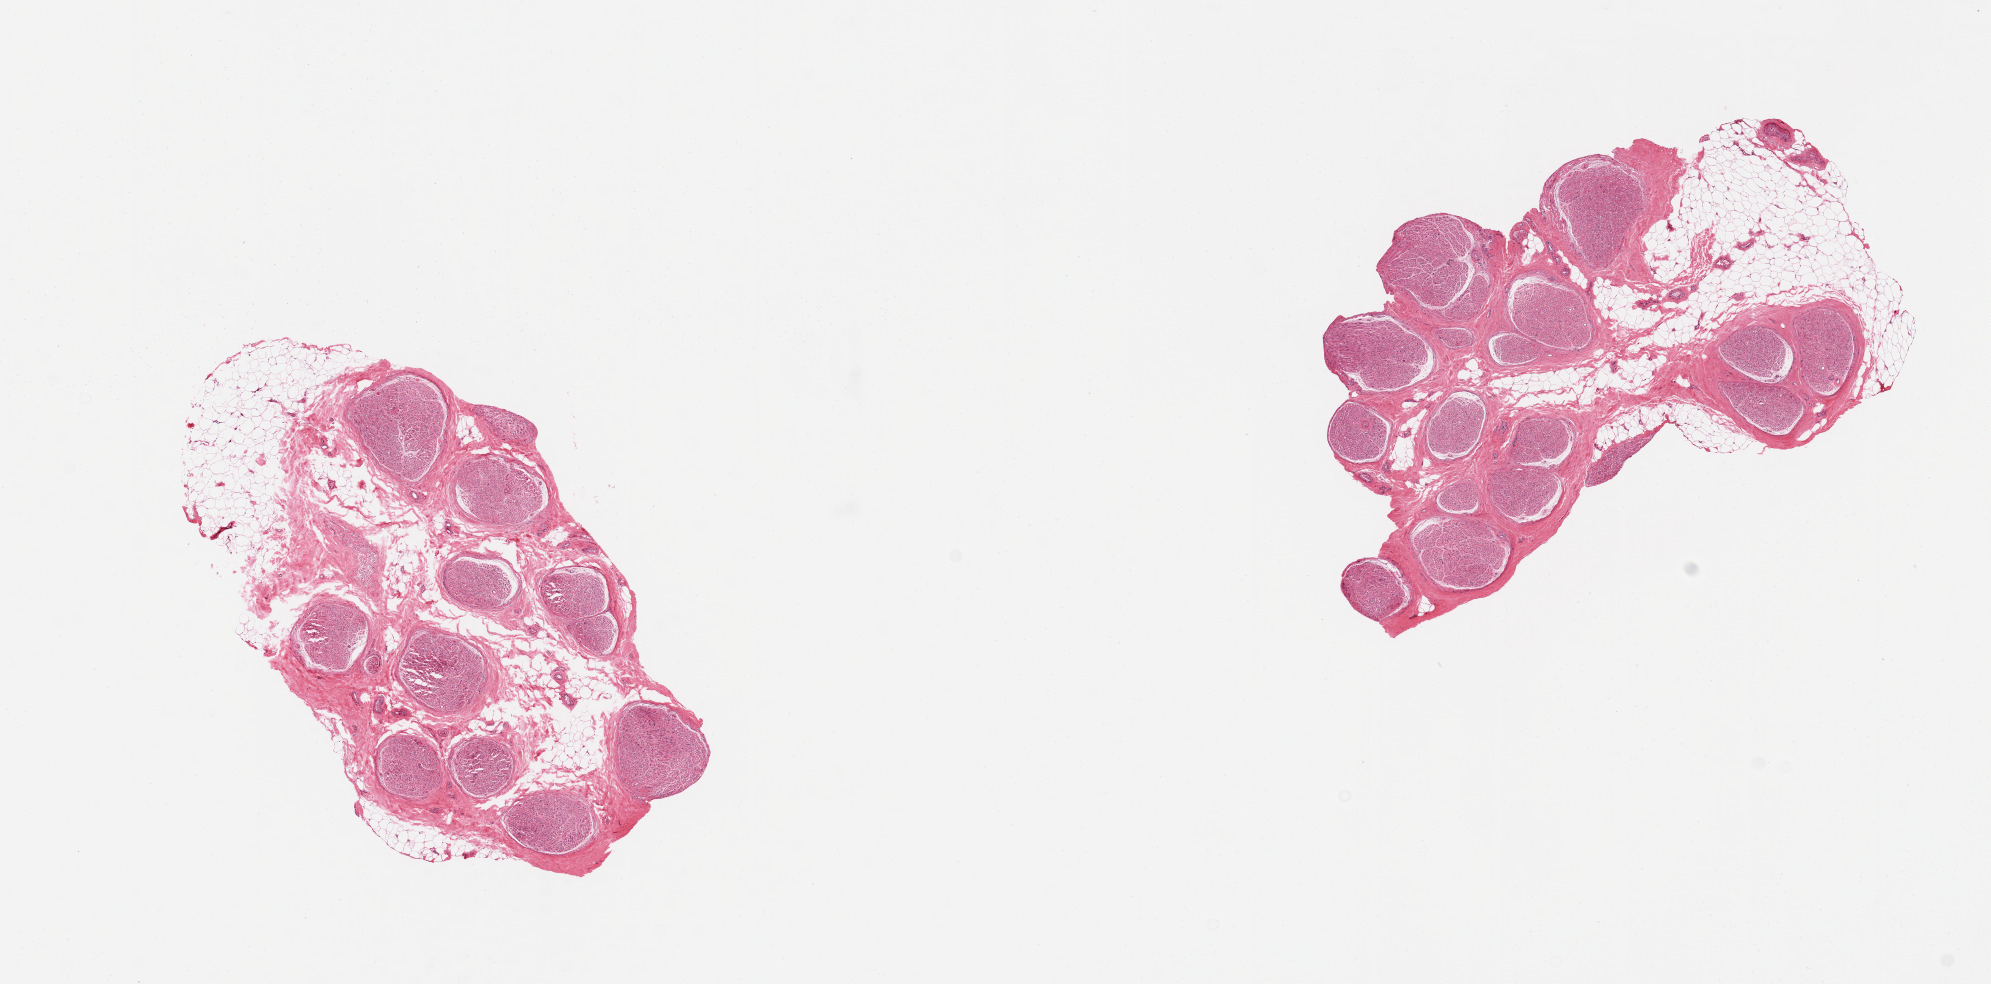
H&E whole-slide image, whole scanned area (about 15.8 x 7.8 mm) shown as a low-resolution overview; PAXgene-fixed, paraffin-embedded tissue; sampled site (target tissue): tibial nerve; donor tissue sample. Donor: male.
Review note (as recorded): 2 pieces, nubbins of adherent fat up to ~1mm.